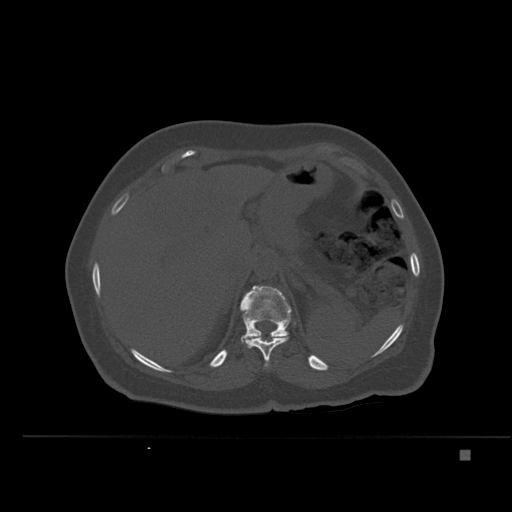
CT including the spine, one axial slice; position 262 of 477 along the scan axis; bone window (W 1800 / L 400 HU); 1.5 mm slice thickness; 512 × 512 image matrix, field of view 422 × 422 mm. Female patient, age 74 years. Case-level facts recorded for this patient, not image findings: primary cancer: colon.
Annotated regions visible in this slice (semi-automatic segmentation, software-assisted and operator-edited):
- T11 vertebra: bounding box <244,335,289,366> (left, top, right, bottom; pixels)
- T12 vertebra: <240,285,292,342>